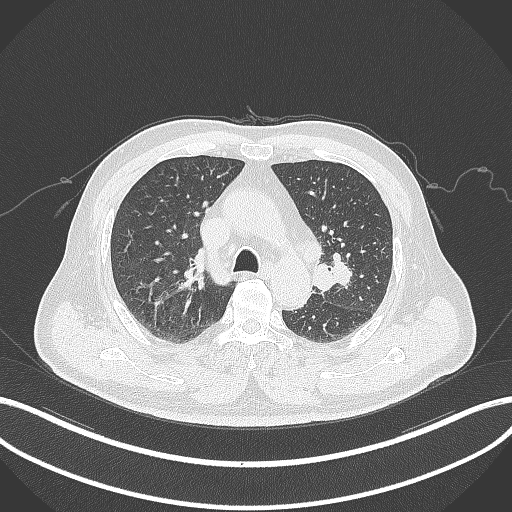
Chest CT, one axial slice. Position 205 of 286 along the scan axis. Reconstruction kernel B70f. Lung window (W 1500 / L -600 HU). 1 mm slice thickness. 512 × 512 image matrix. Patient: male, 67 years. From the clinical record (not read from this slice): clinical TNM (as recorded): T2a N1 M0.
Annotated regions visible in this slice (bounding box drawn by a radiologist):
- lung tumour (recorded histology: adenocarcinoma): bounding box [x1, y1, x2, y2] px = [311, 252, 355, 293]